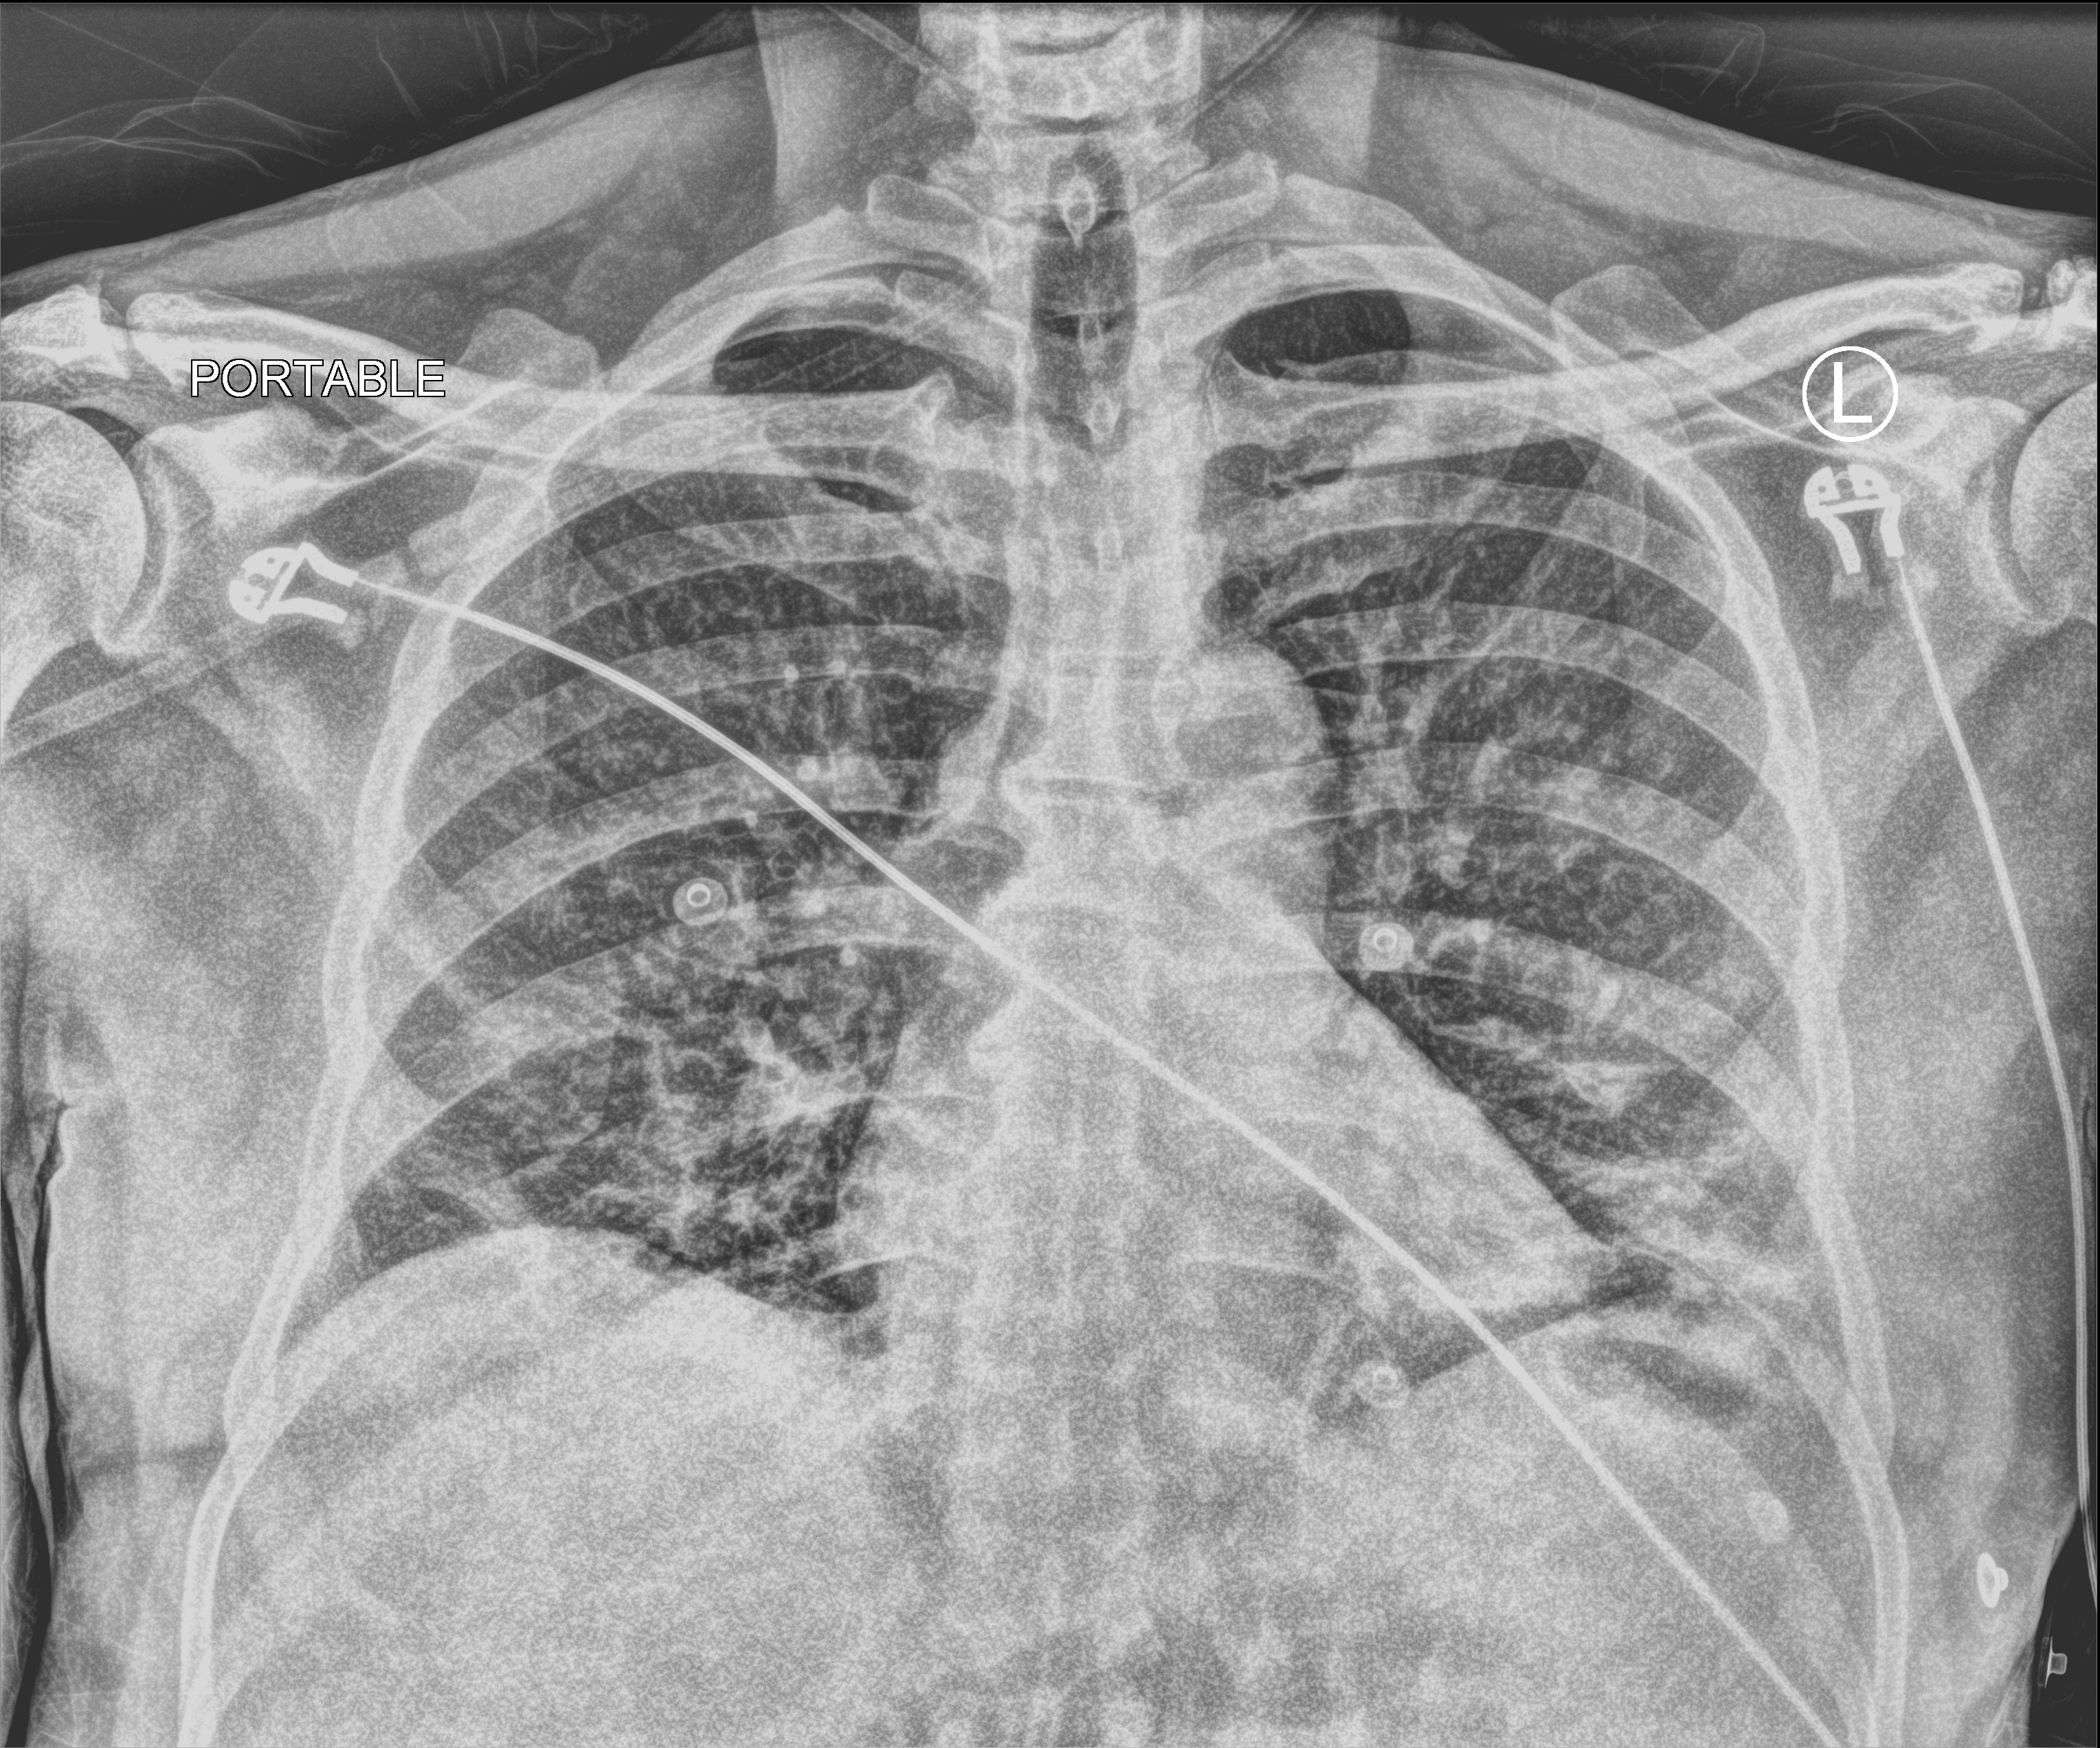
Portable chest radiograph, anteroposterior (AP) projection. Patient hospitalised with COVID-19; male, aged 18–59 years.
From the hospital-stay record, not from the radiograph (when in the stay this image was taken is not recorded): mechanically ventilated during this hospital stay: no; admitted to intensive care during this hospital stay: no.